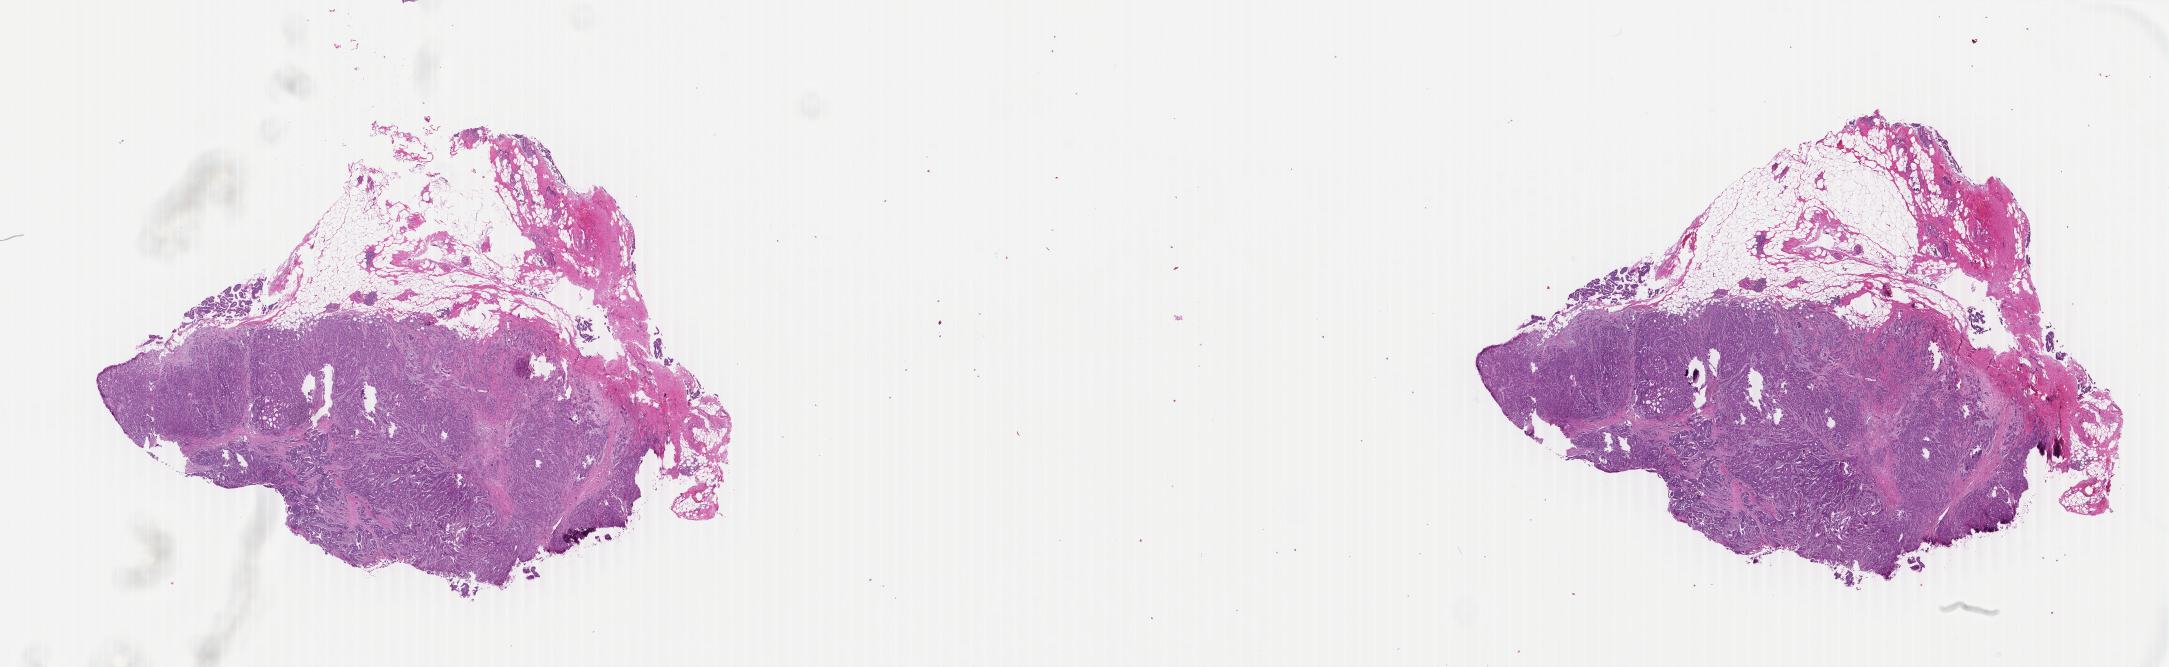
Whole-slide histology image, H&E-stained, whole scanned area (about 34.5 x 10.6 mm) shown as a low-resolution overview; formalin-fixed paraffin-embedded (FFPE) diagnostic section; sample: primary tumour, breast. Female, age 62 years at initial diagnosis.
Laterality: right. Pathologic diagnosis: Infiltrating duct carcinoma, NOS. AJCC pathologic stage: IA (6th edition). Lymph nodes positive (case pathology): 0 of 1 examined.